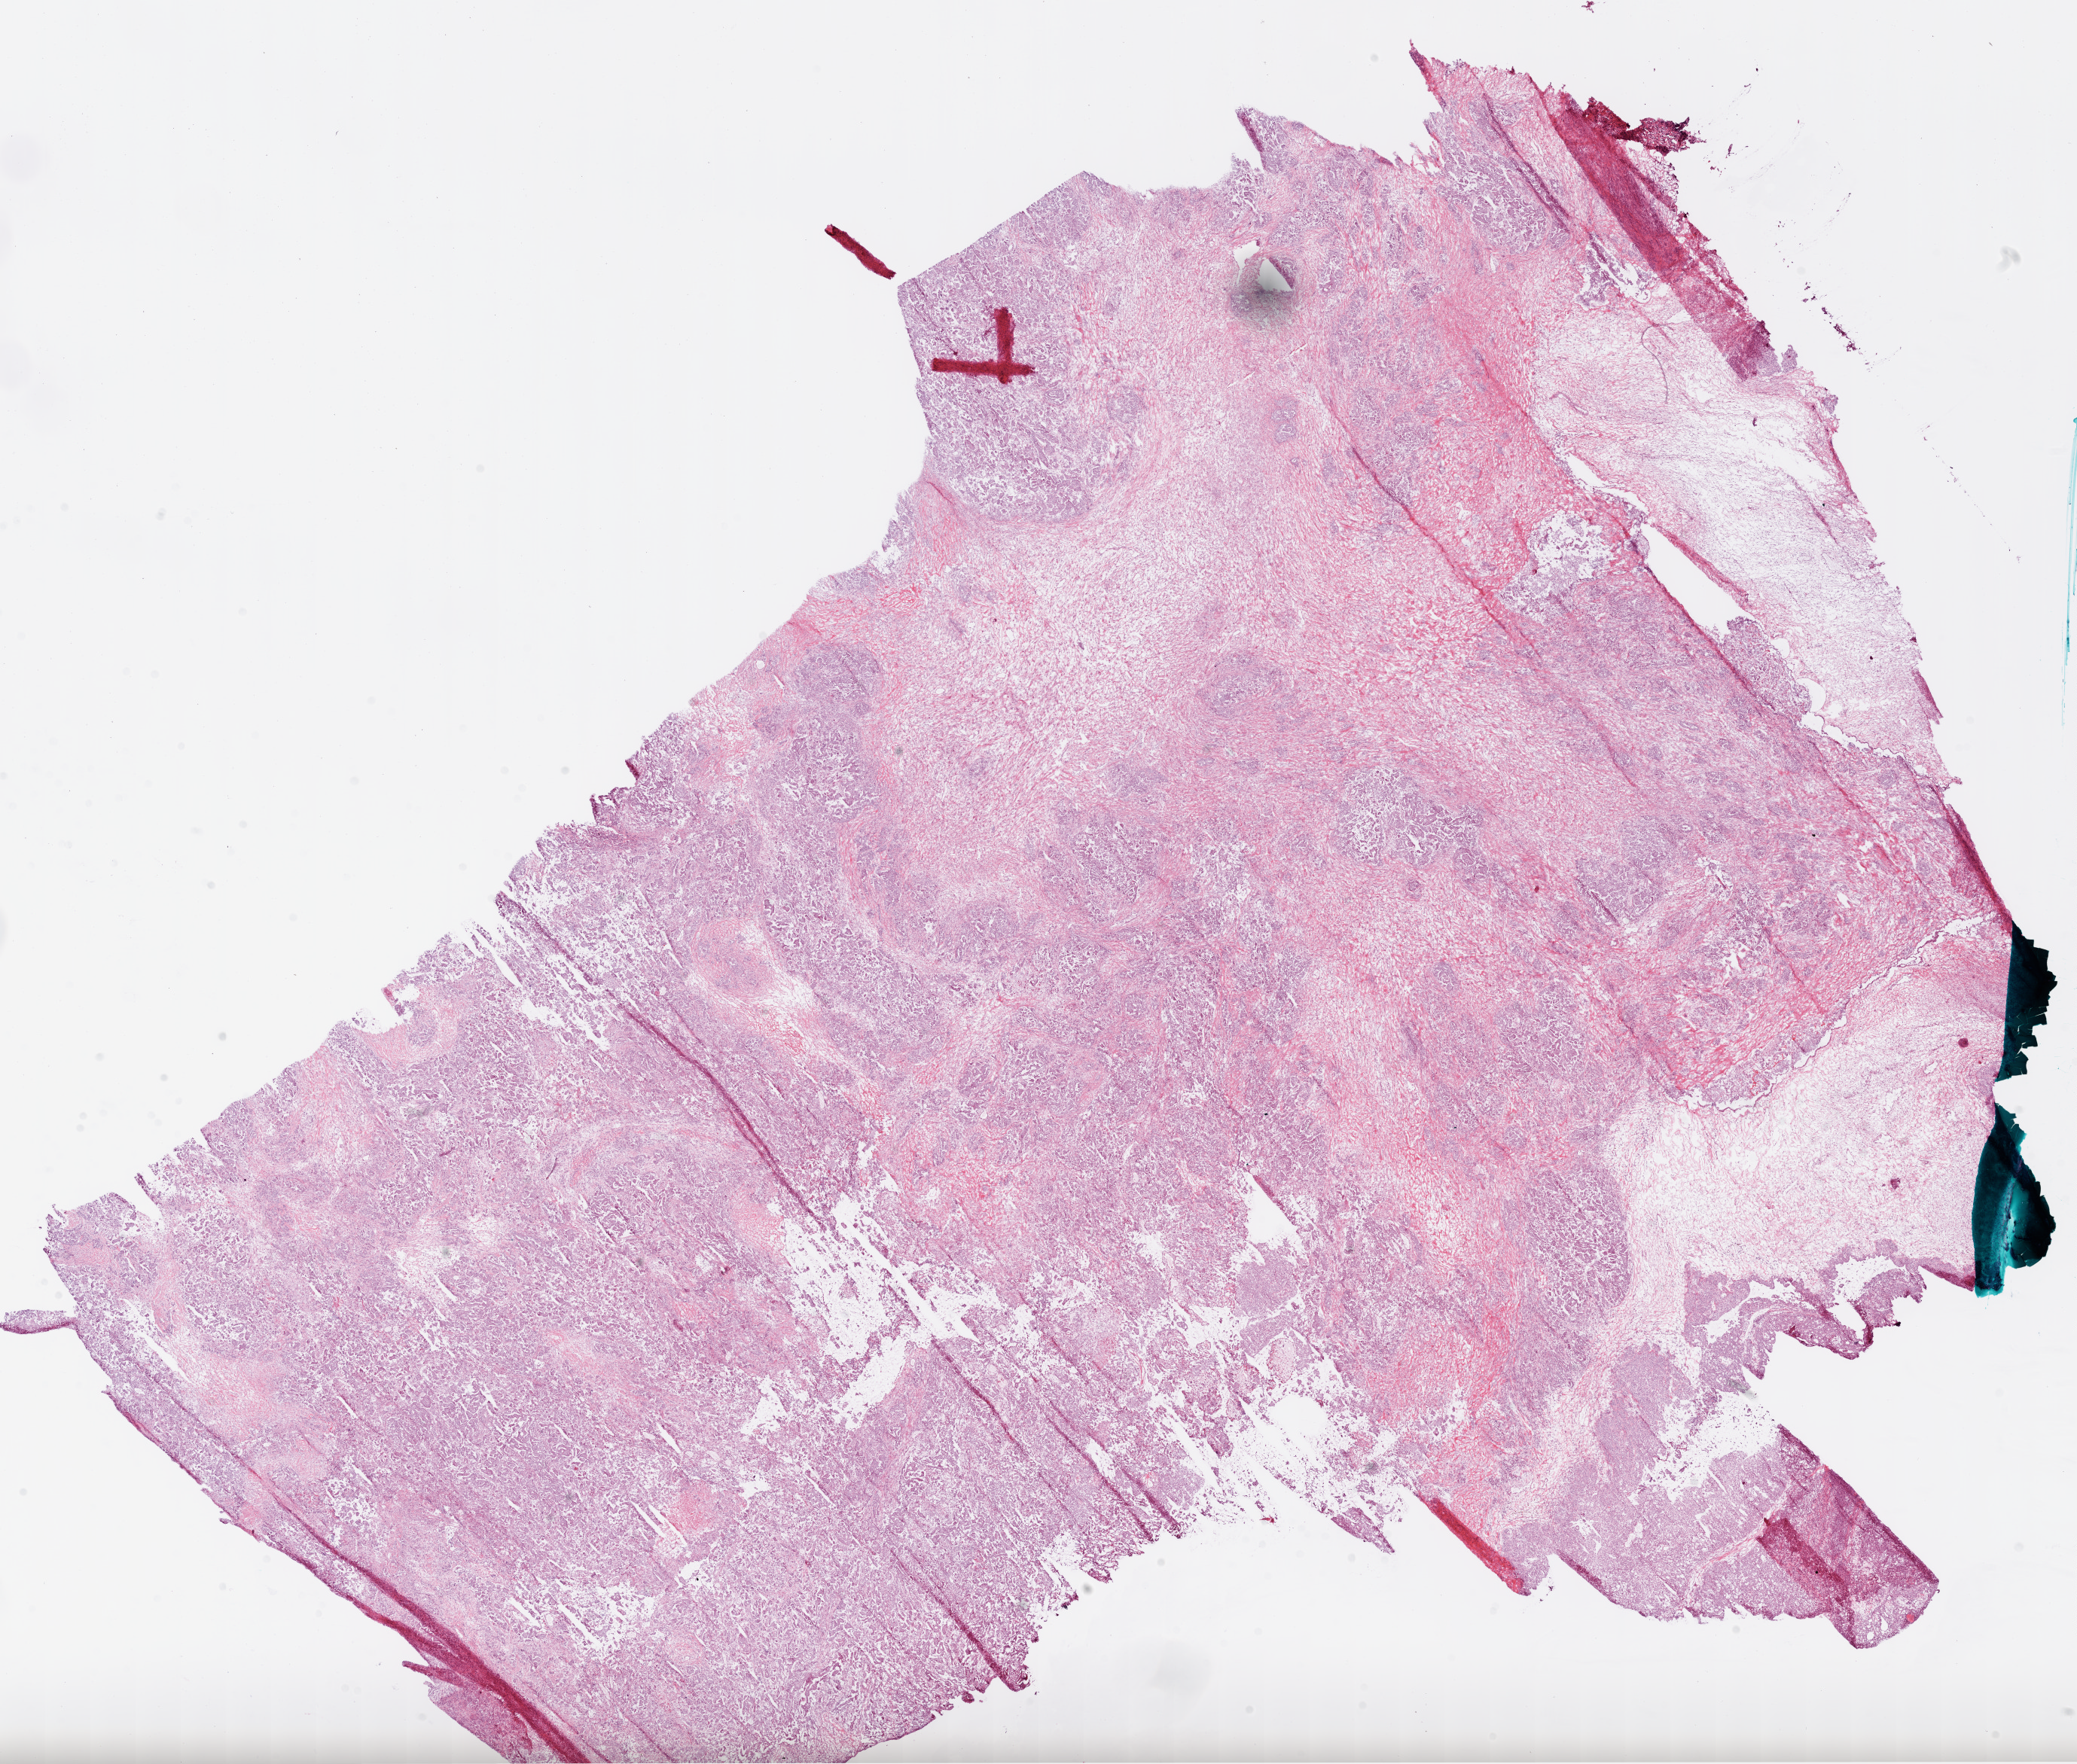
Digitized H&E-stained tissue section (whole slide), low-resolution overview of the scanned area, about 22.2 x 18.9 mm (acquisition: 20x scan); frozen section from the bottom of the tissue portion; sample: primary tumour, ovary. Female patient; age at initial diagnosis 61 years. Pathologist review of this section (percent, as recorded): tumour cells 60%, tumour nuclei 85%.
Histologic diagnosis: Serous cystadenocarcinoma, NOS.